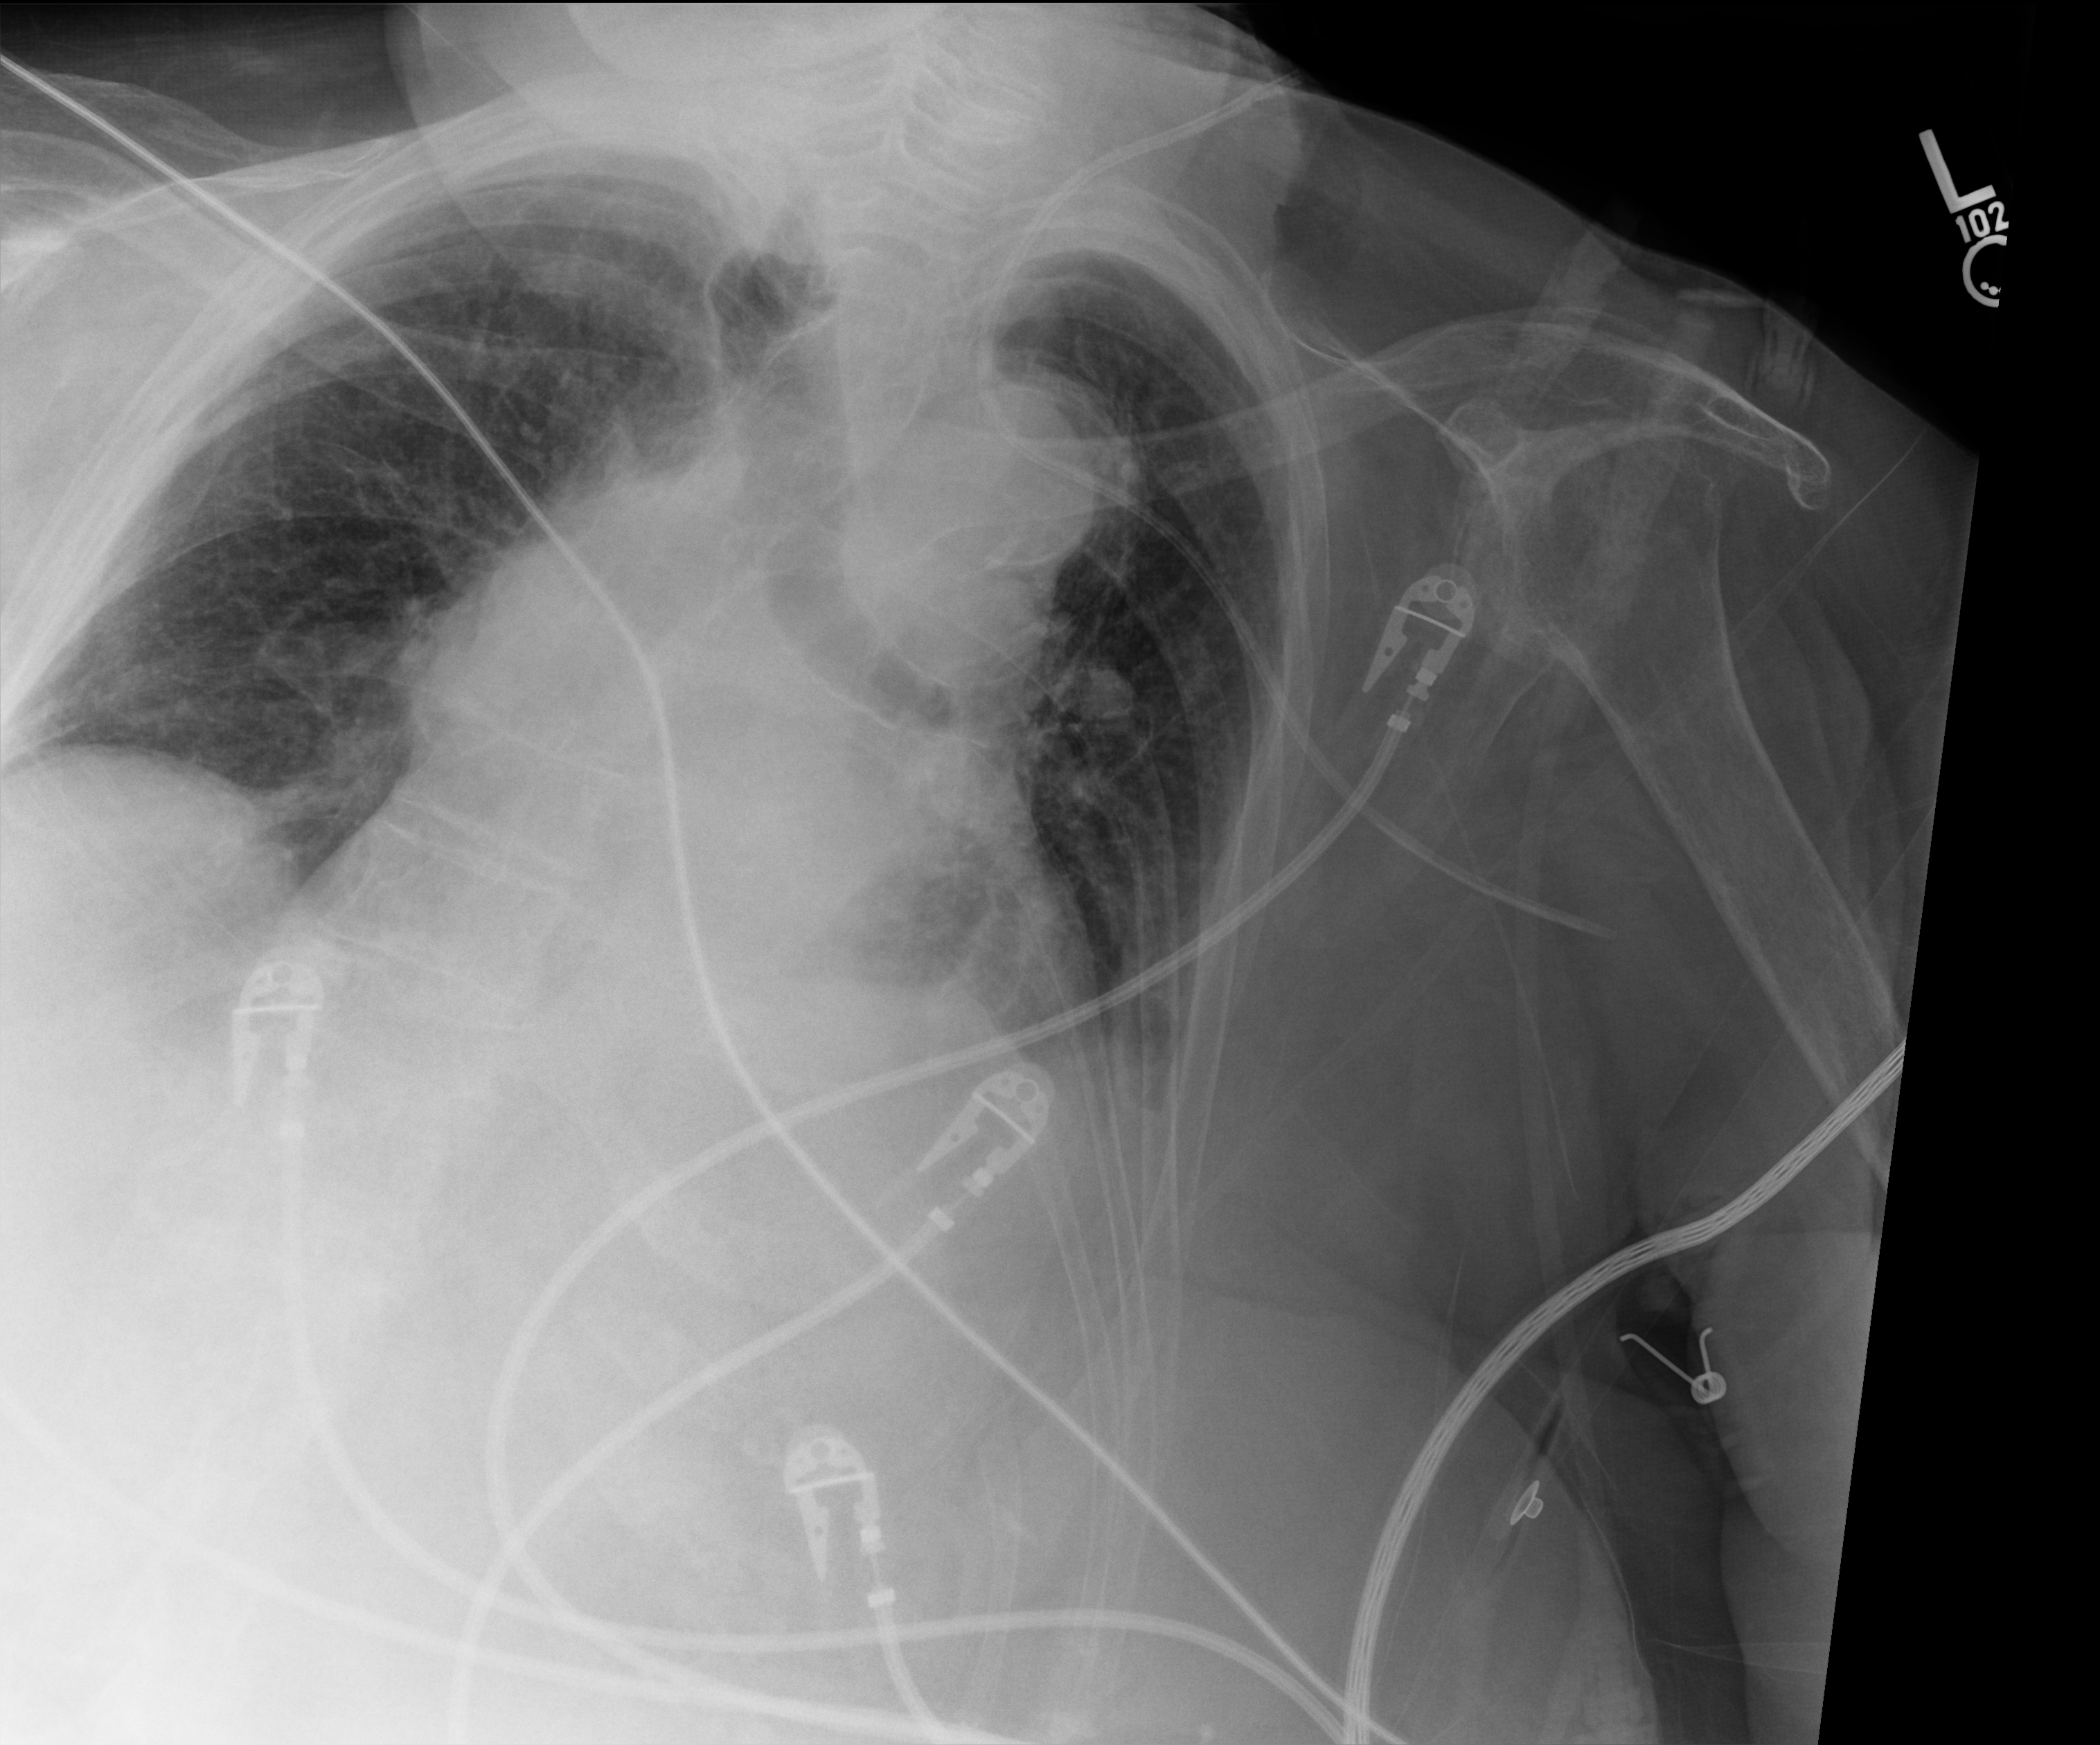
Chest X-ray (portable). Patient hospitalised with COVID-19; female, aged 75–90 years.
From the hospital-stay record, not from the radiograph (when in the stay this image was taken is not recorded):
- length of hospital stay: 12 days
- admitted to intensive care during this hospital stay: yes